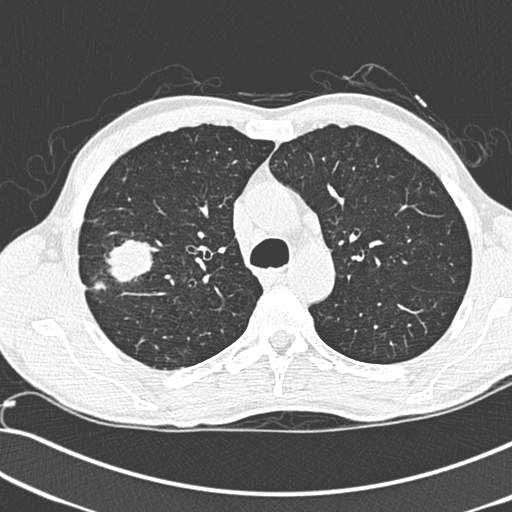
Low-dose screening chest CT, one axial slice; slice 209 of 281 in the series (ordered by position); lung window (W 1500 / L -600 HU); 1.3 mm slice thickness; 512 × 512 image matrix, field of view 341 × 341 mm.
Annotated regions visible in this slice (expert manual segmentation):
- lesion 1 (tumor, upper lobe of right lung): box from (x=93, y=240) to (x=154, y=295) px